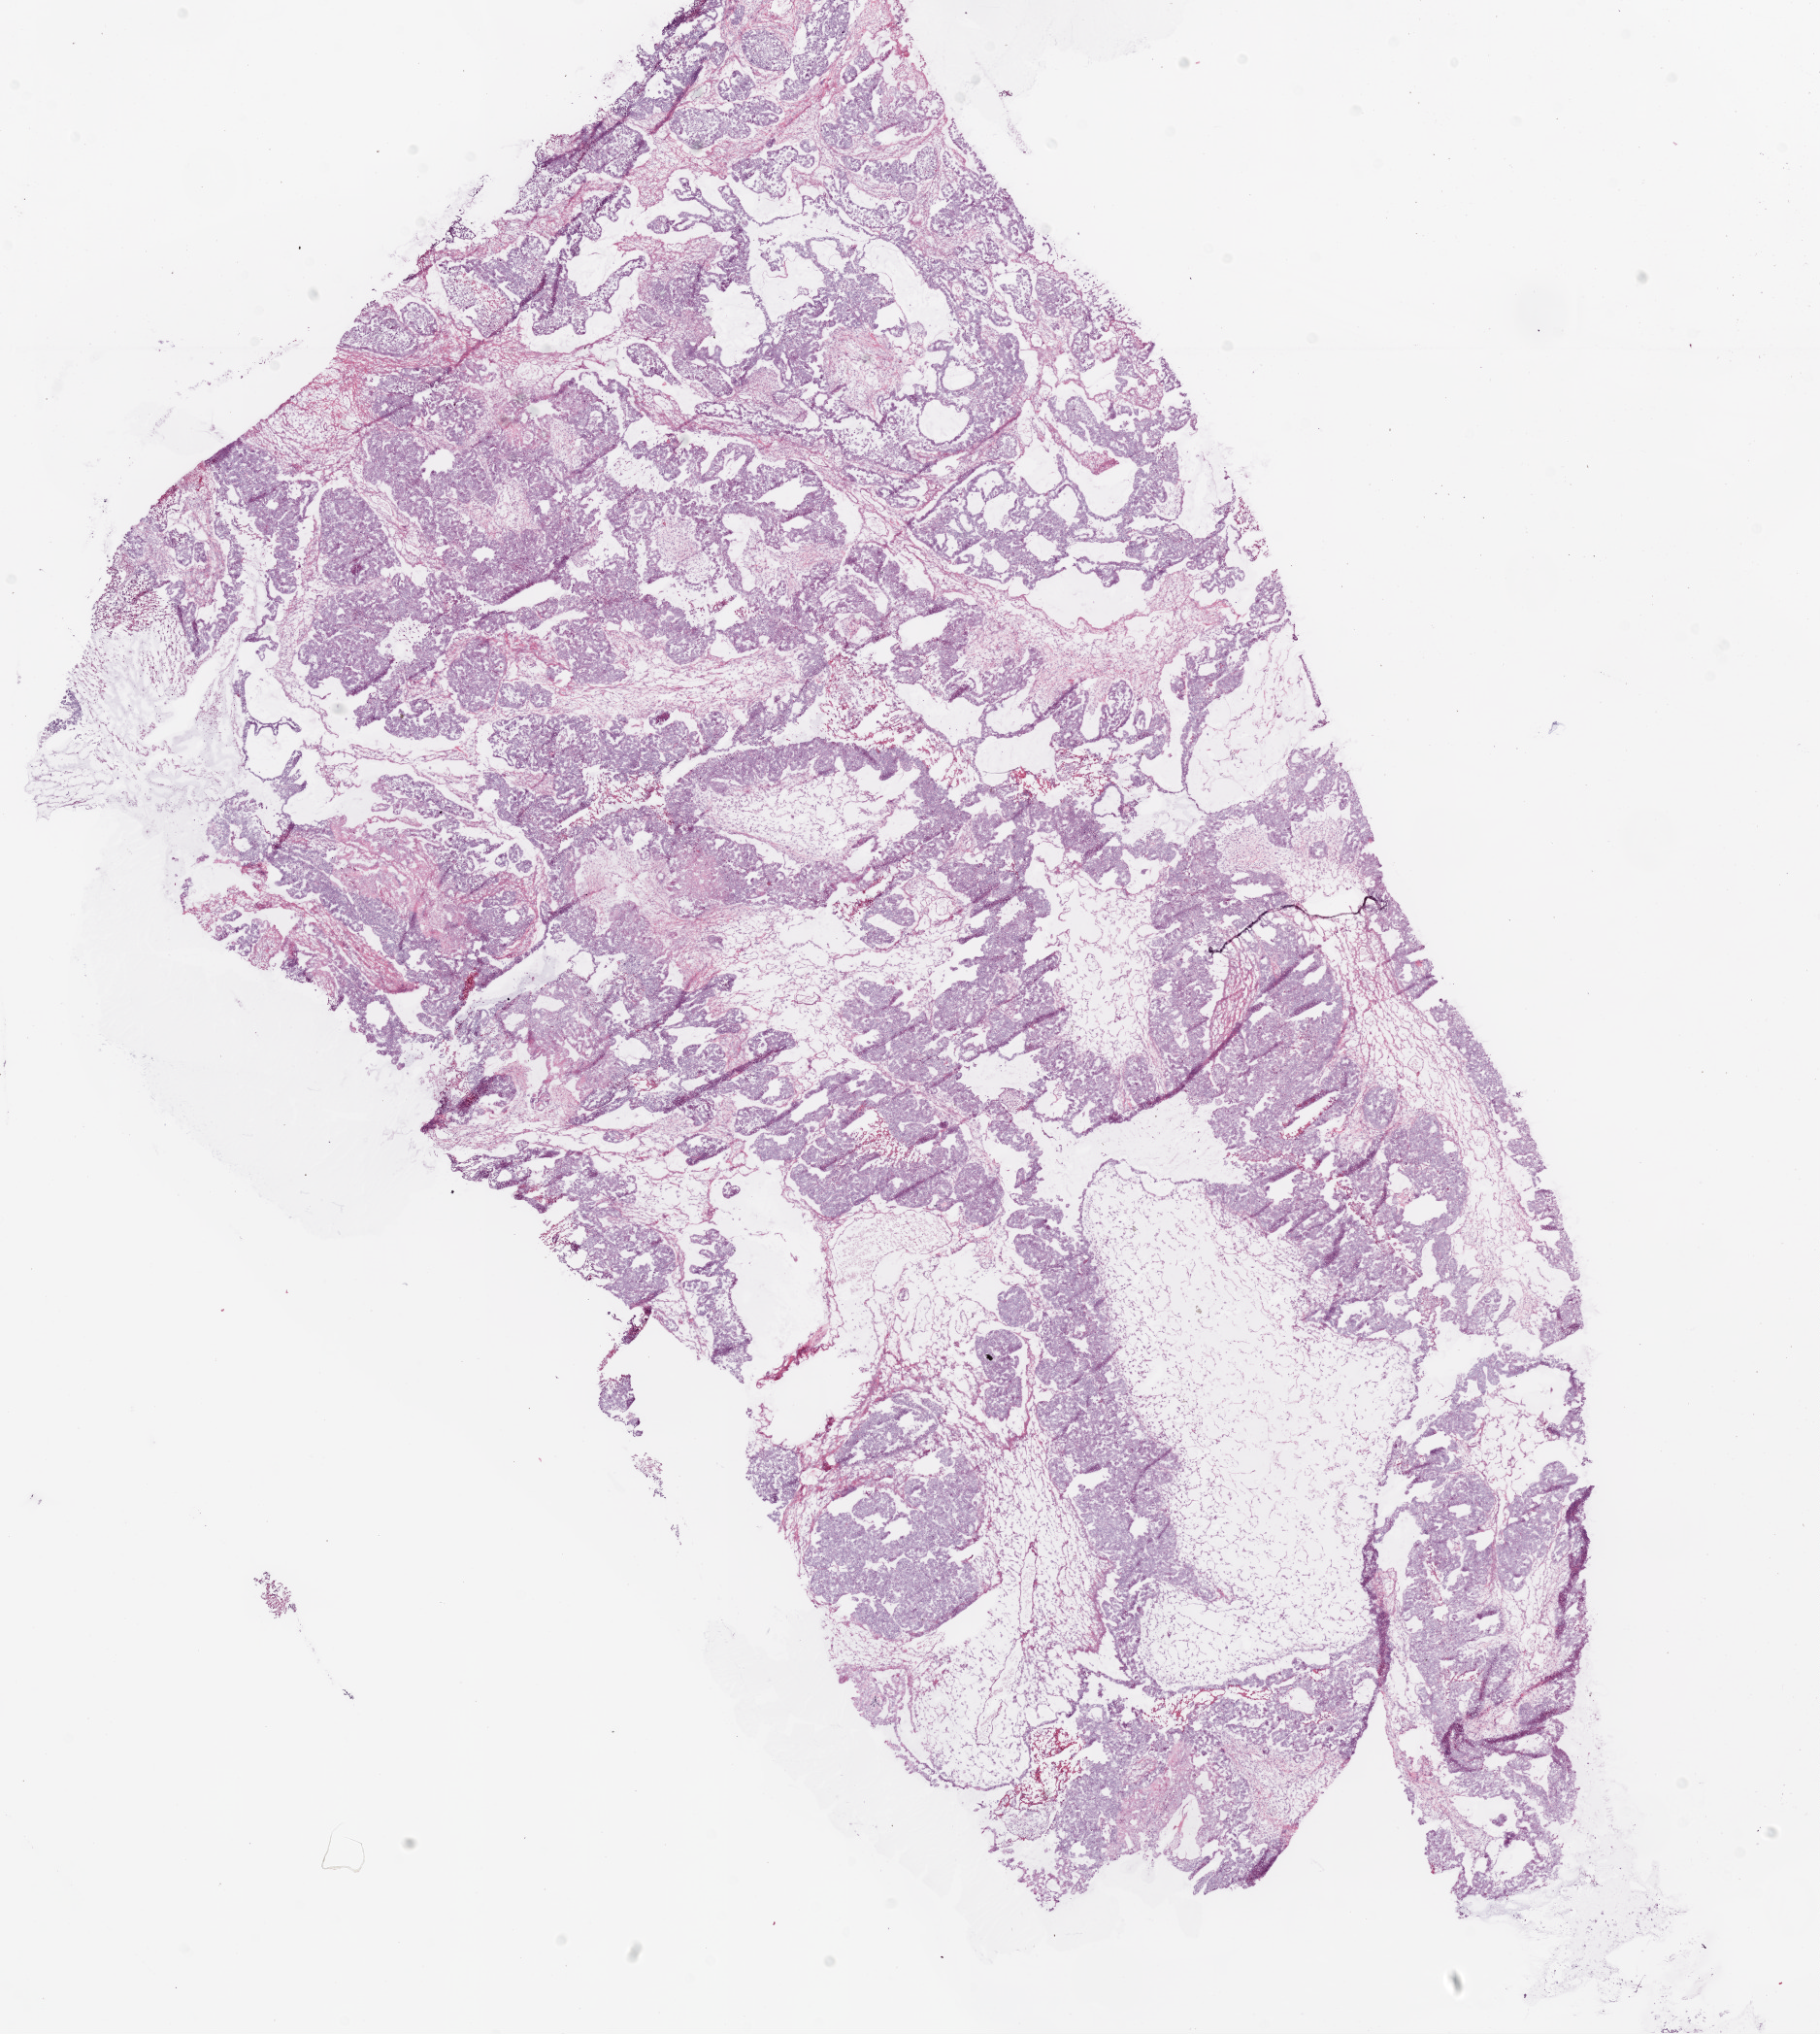
Whole-slide histology image, H&E — whole scanned area (about 15.0 x 16.8 mm, from a 20x scan) shown as a low-resolution overview. Frozen section from the bottom of the tissue portion. Primary tumour sample from the ovary. Female patient; age at initial diagnosis 62 years. Histologic grade: G2 (moderately differentiated). Slide review estimates, as recorded: tumour cells 80%, tumour nuclei 80%, normal cells 0%, stromal cells 20%, necrosis 0%.
Laterality: bilateral. FIGO stage: IIIC. Pathologic diagnosis: Serous cystadenocarcinoma, NOS.